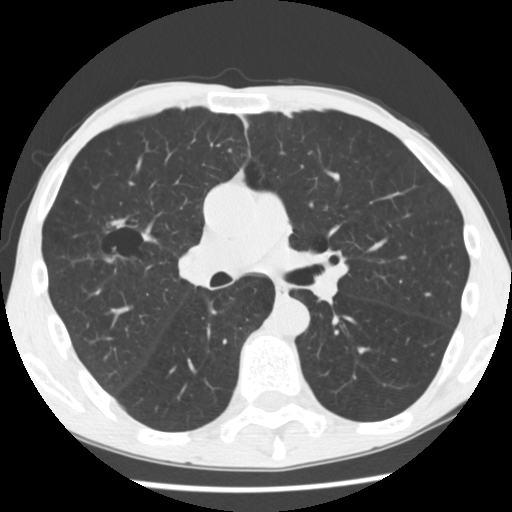
Axial slice from a low-dose chest CT screening exam. First (baseline) screen. Lung window (W 1500 / L -600 HU). 2.5 mm slice thickness. Standard (soft-tissue) reconstruction kernel (STANDARD). Male participant, aged 56 years at enrolment. Current smoker at enrolment.
Lesion marked by an expert reader, bounding box <94,206,156,260> (left, top, right, bottom; pixels). The screening reader recorded 2 non-calcified nodules or masses ≥4 mm on this exam; which of them this box marks is not recorded.